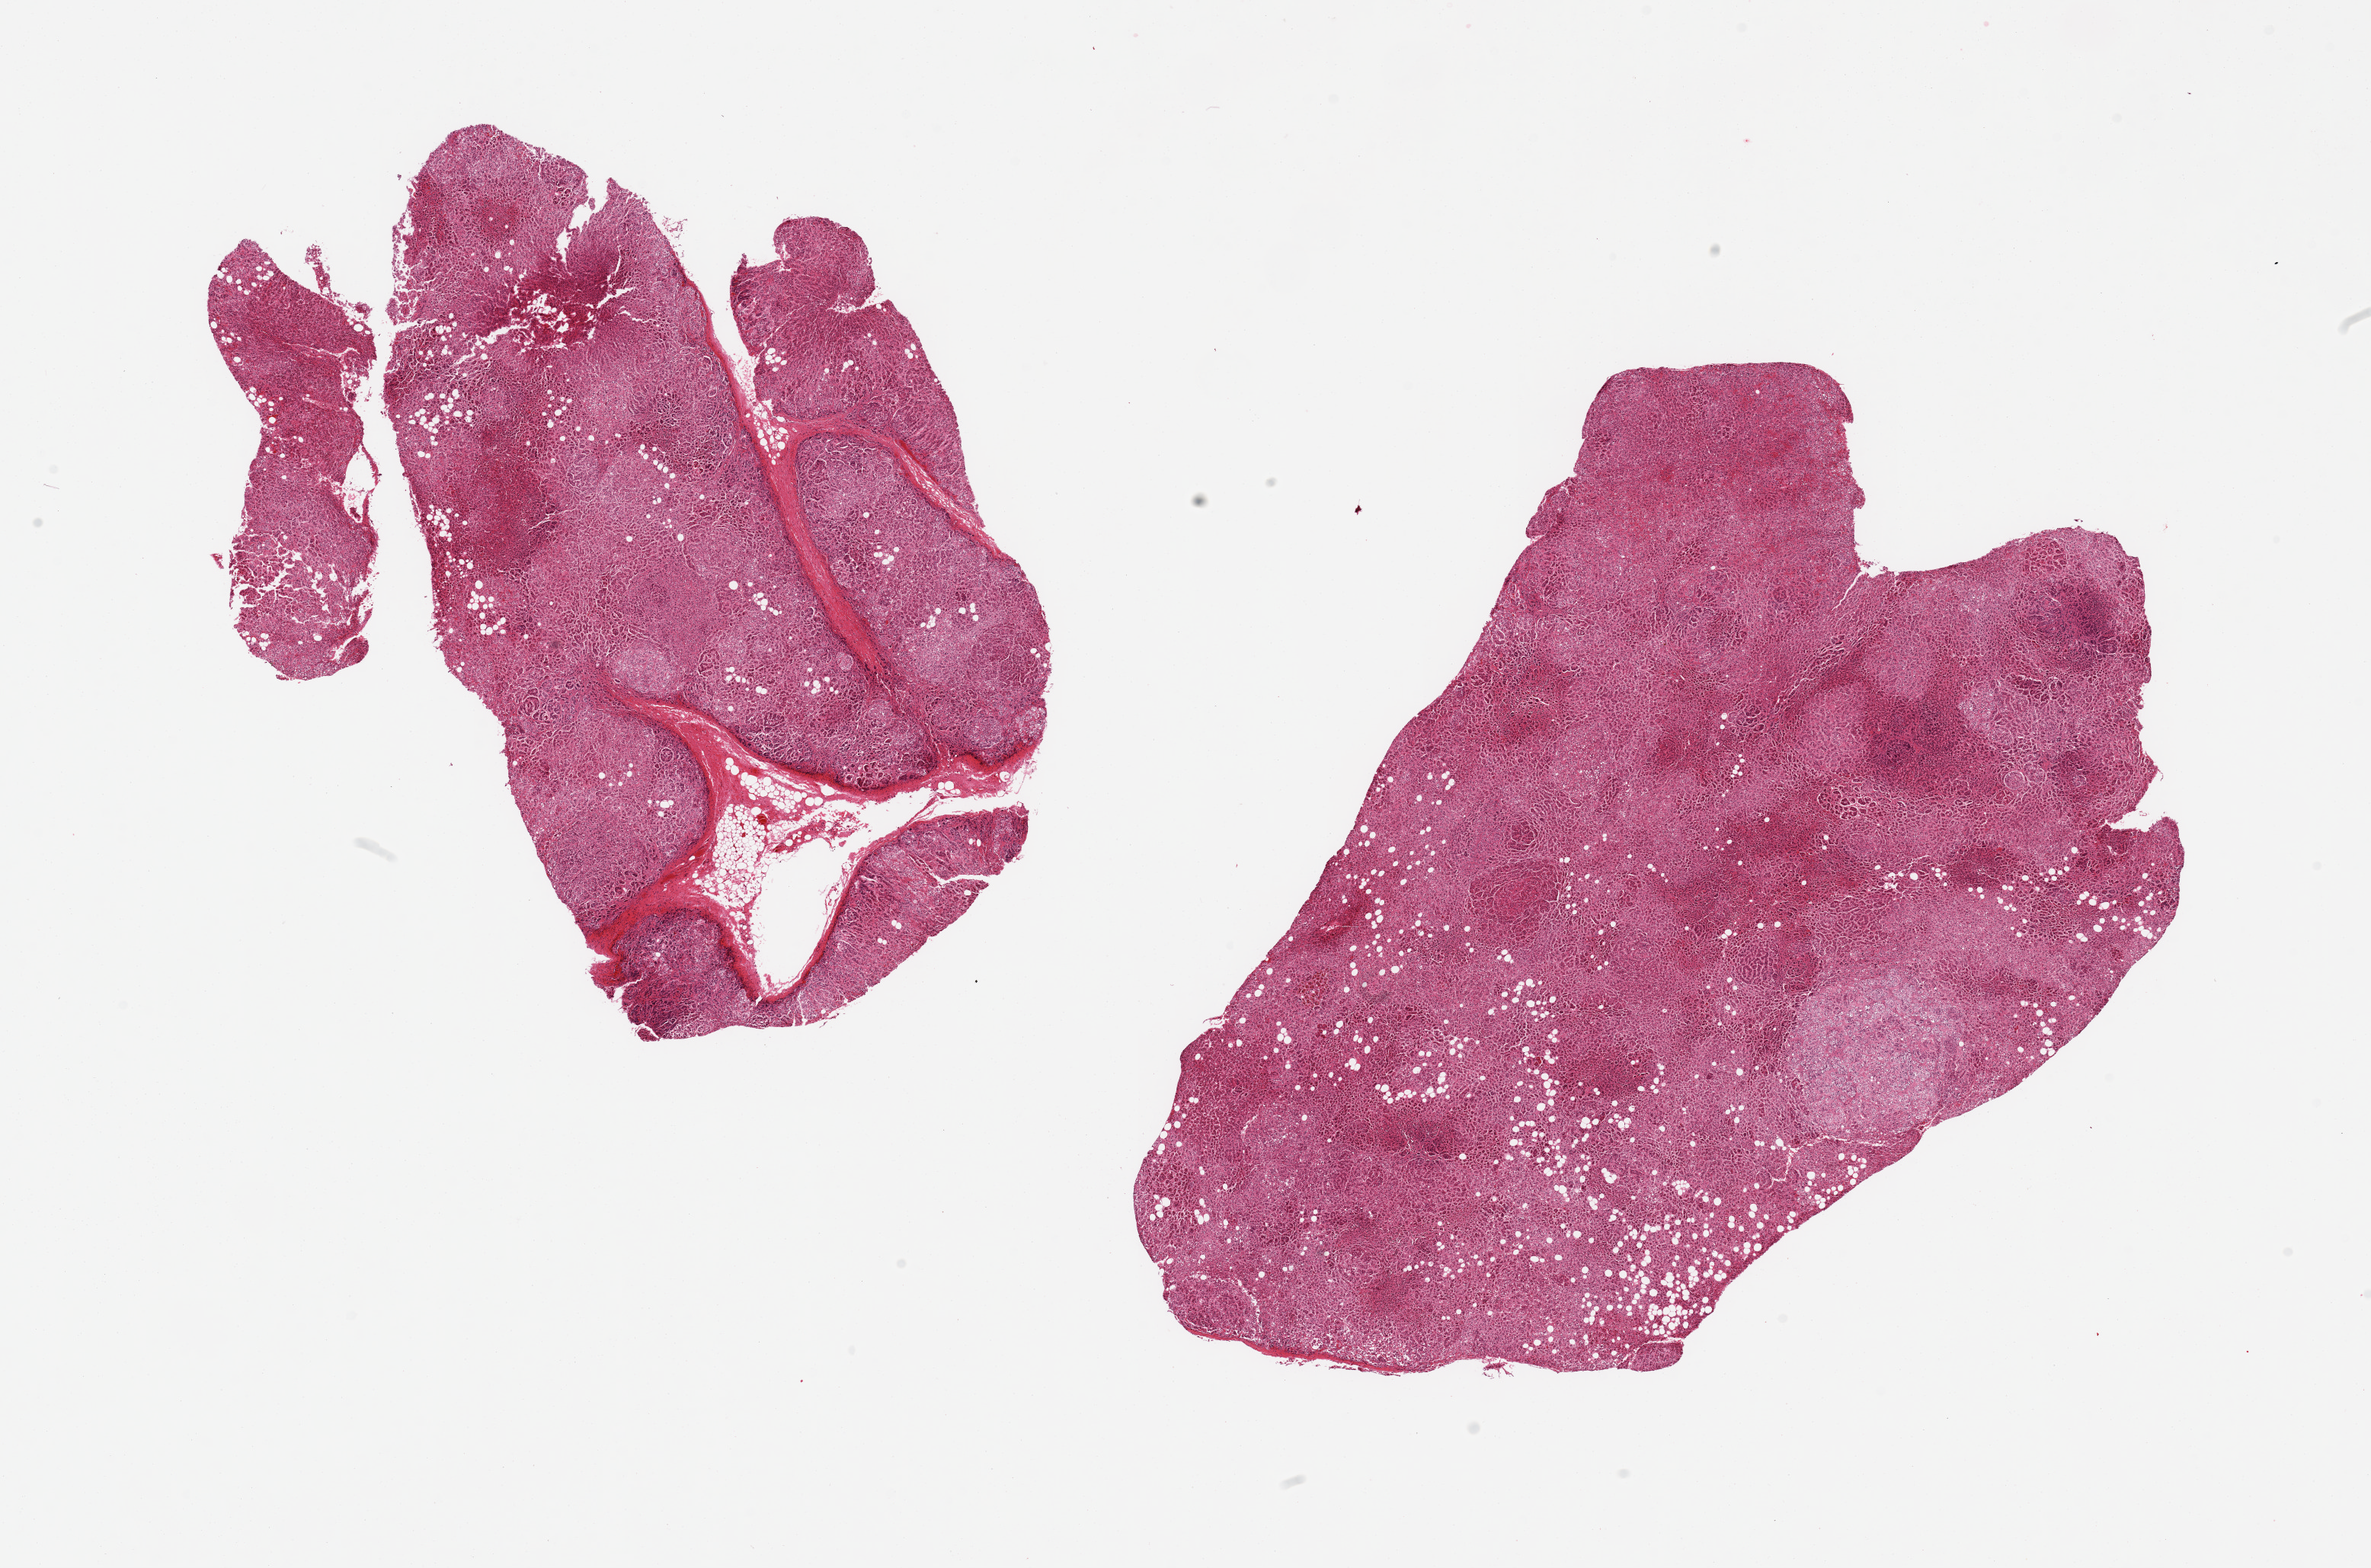
Whole-slide image, hematoxylin and eosin (H&E) stain — whole scanned area (about 24.6 x 16.3 mm) shown as a low-resolution overview, PAXgene-fixed, paraffin-embedded tissue, section of adrenal gland (target tissue), donor tissue sample. Donor sex: male.
Reviewer comment on this tissue sample: 2 pieces; 5% internal fat.